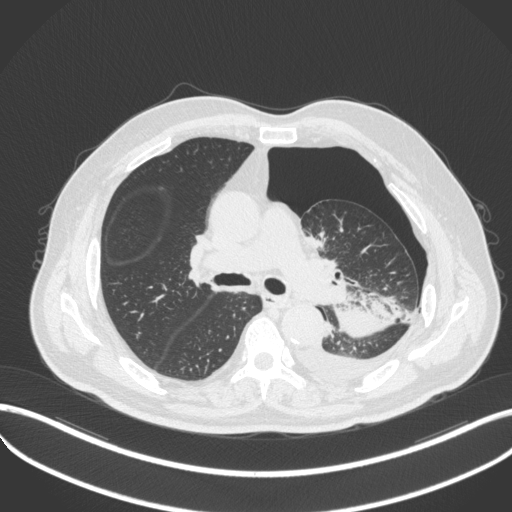
Chest CT, one axial slice; position 317 of 466 along the scan axis; reconstruction kernel B31f; lung window (W 1500 / L -600 HU); 1 mm slice thickness; 512 × 512 image matrix, field of view 400 × 400 mm. Patient: male, 76 years. From the clinical record (not read from this slice): clinical TNM (as recorded): T3 N0 M1b.
Structures marked on this image (rectangle marked by the reading radiologist):
- lung tumour (recorded histology: adenocarcinoma): bounding box [x1, y1, x2, y2] px = [332, 278, 404, 338]